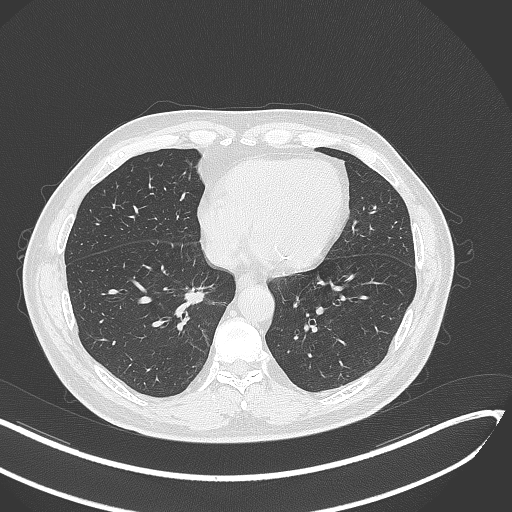
Chest CT, one axial slice. Position 133 of 429 along the scan axis. 120 kVp. Lung window (W 1500 / L -600 HU). 1 mm slice thickness. 512 × 512 image matrix, field of view 400 × 400 mm. Patient: male, 62 years. From the clinical record (not read from this slice): clinical TNM (as recorded): T1b N0 M0; histopathological grade: G2.
Outlined on this slice (bounding box drawn by a radiologist):
- lung tumour (recorded histology: adenocarcinoma): bounding box [x1, y1, x2, y2] px = [181, 286, 209, 307]